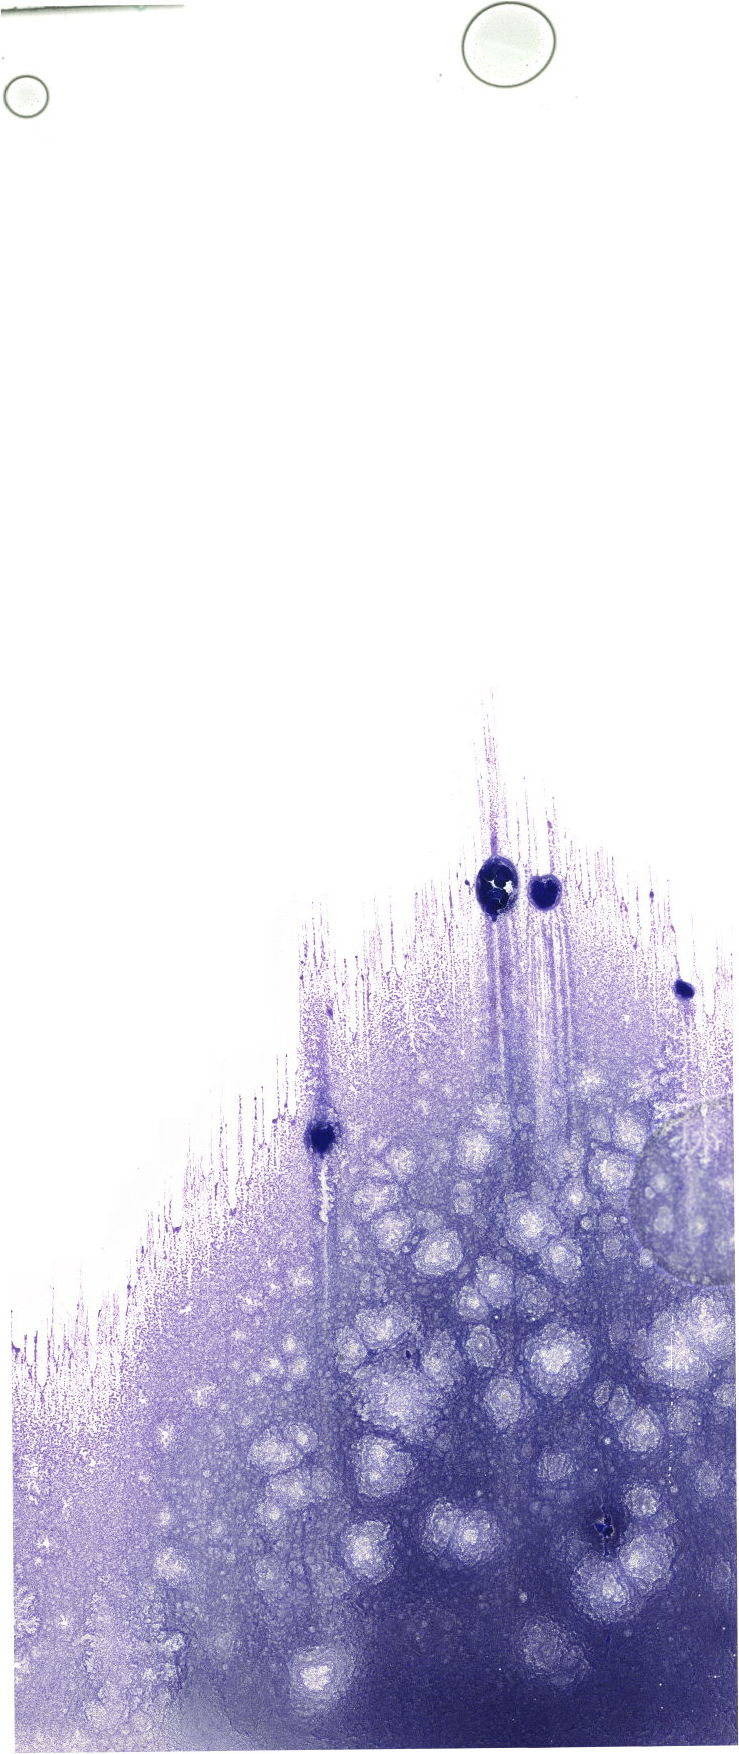
May-Grünwald–Giemsa-stained marrow aspirate smear (whole slide) — shown as a low-resolution overview of the whole scanned area (about 20.9 x 49.7 mm). Patient sex: male.
Diagnosis: Chronic Phase Chronic Myeloid Leukemia, BCR-ABL1 Positive.